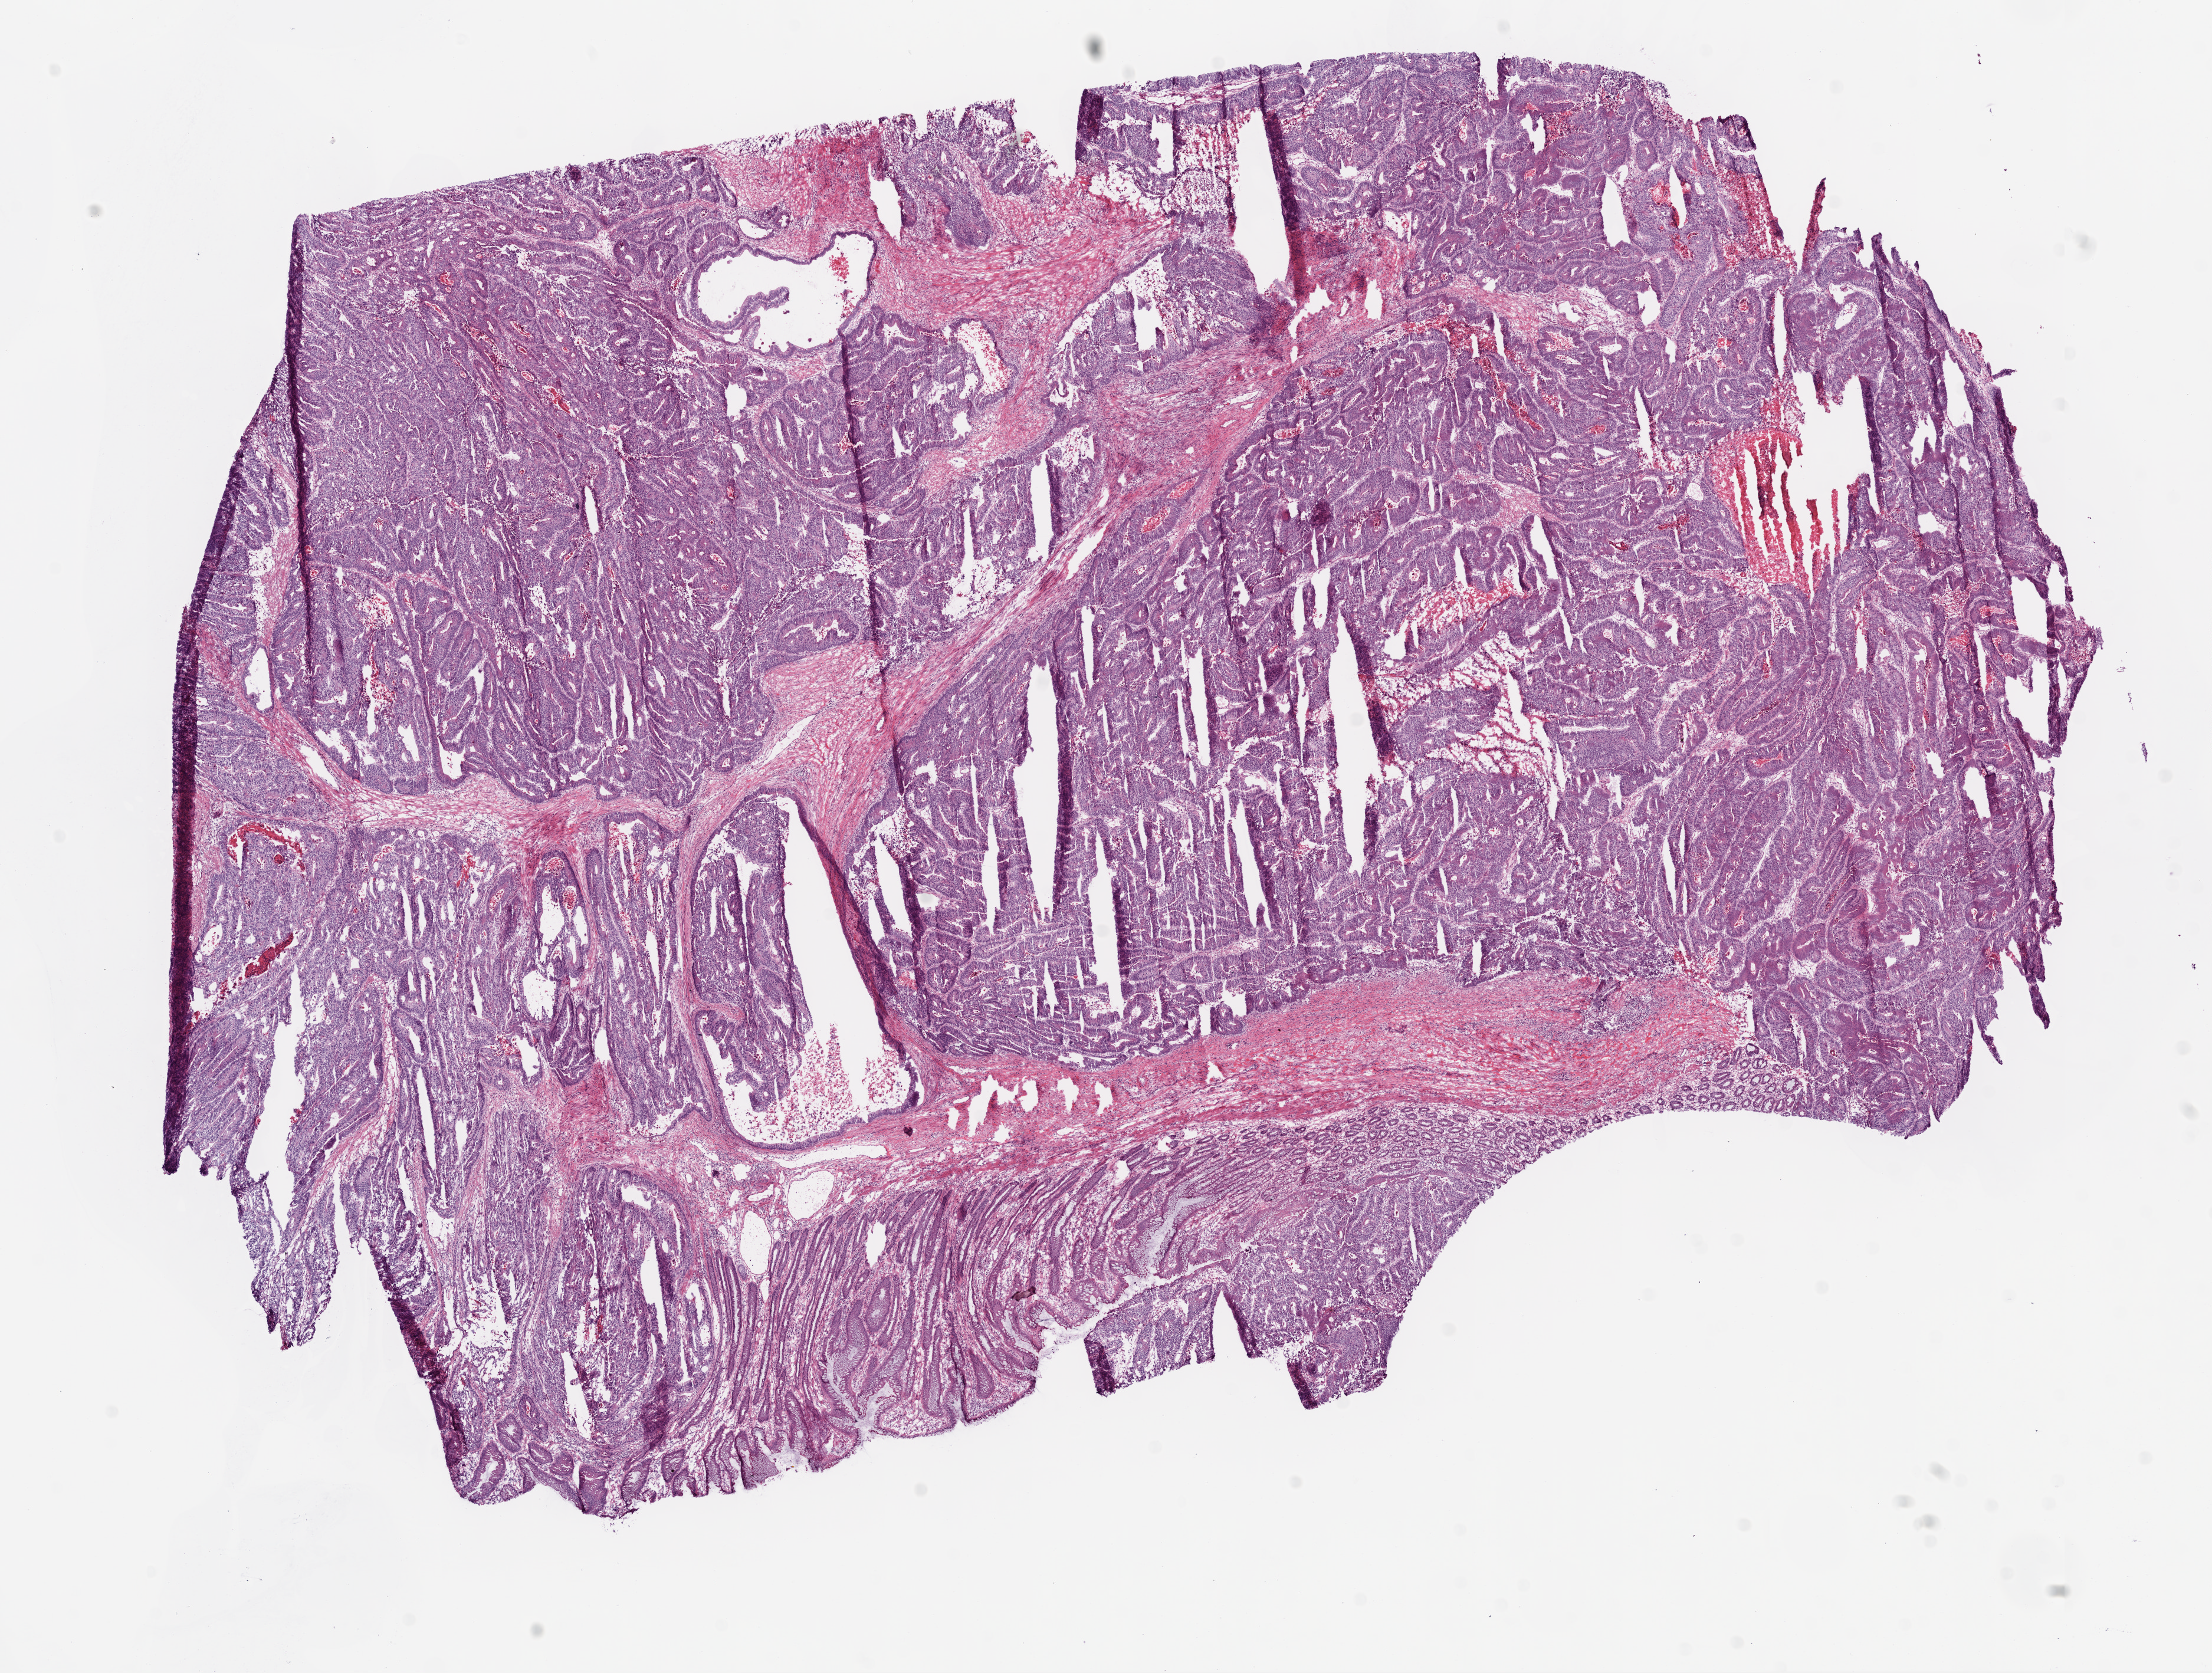
Whole-slide histology image, Hematoxylin and eosin (H&E) stained — a low-resolution overview of the entire scanned area, about 15.0 x 11.4 mm (slide scanned at 20x), frozen section, sample: primary tumour, colon. Patient: female, age at initial diagnosis 75 years.
Histologic diagnosis: Adenocarcinoma, NOS (sigmoid colon).